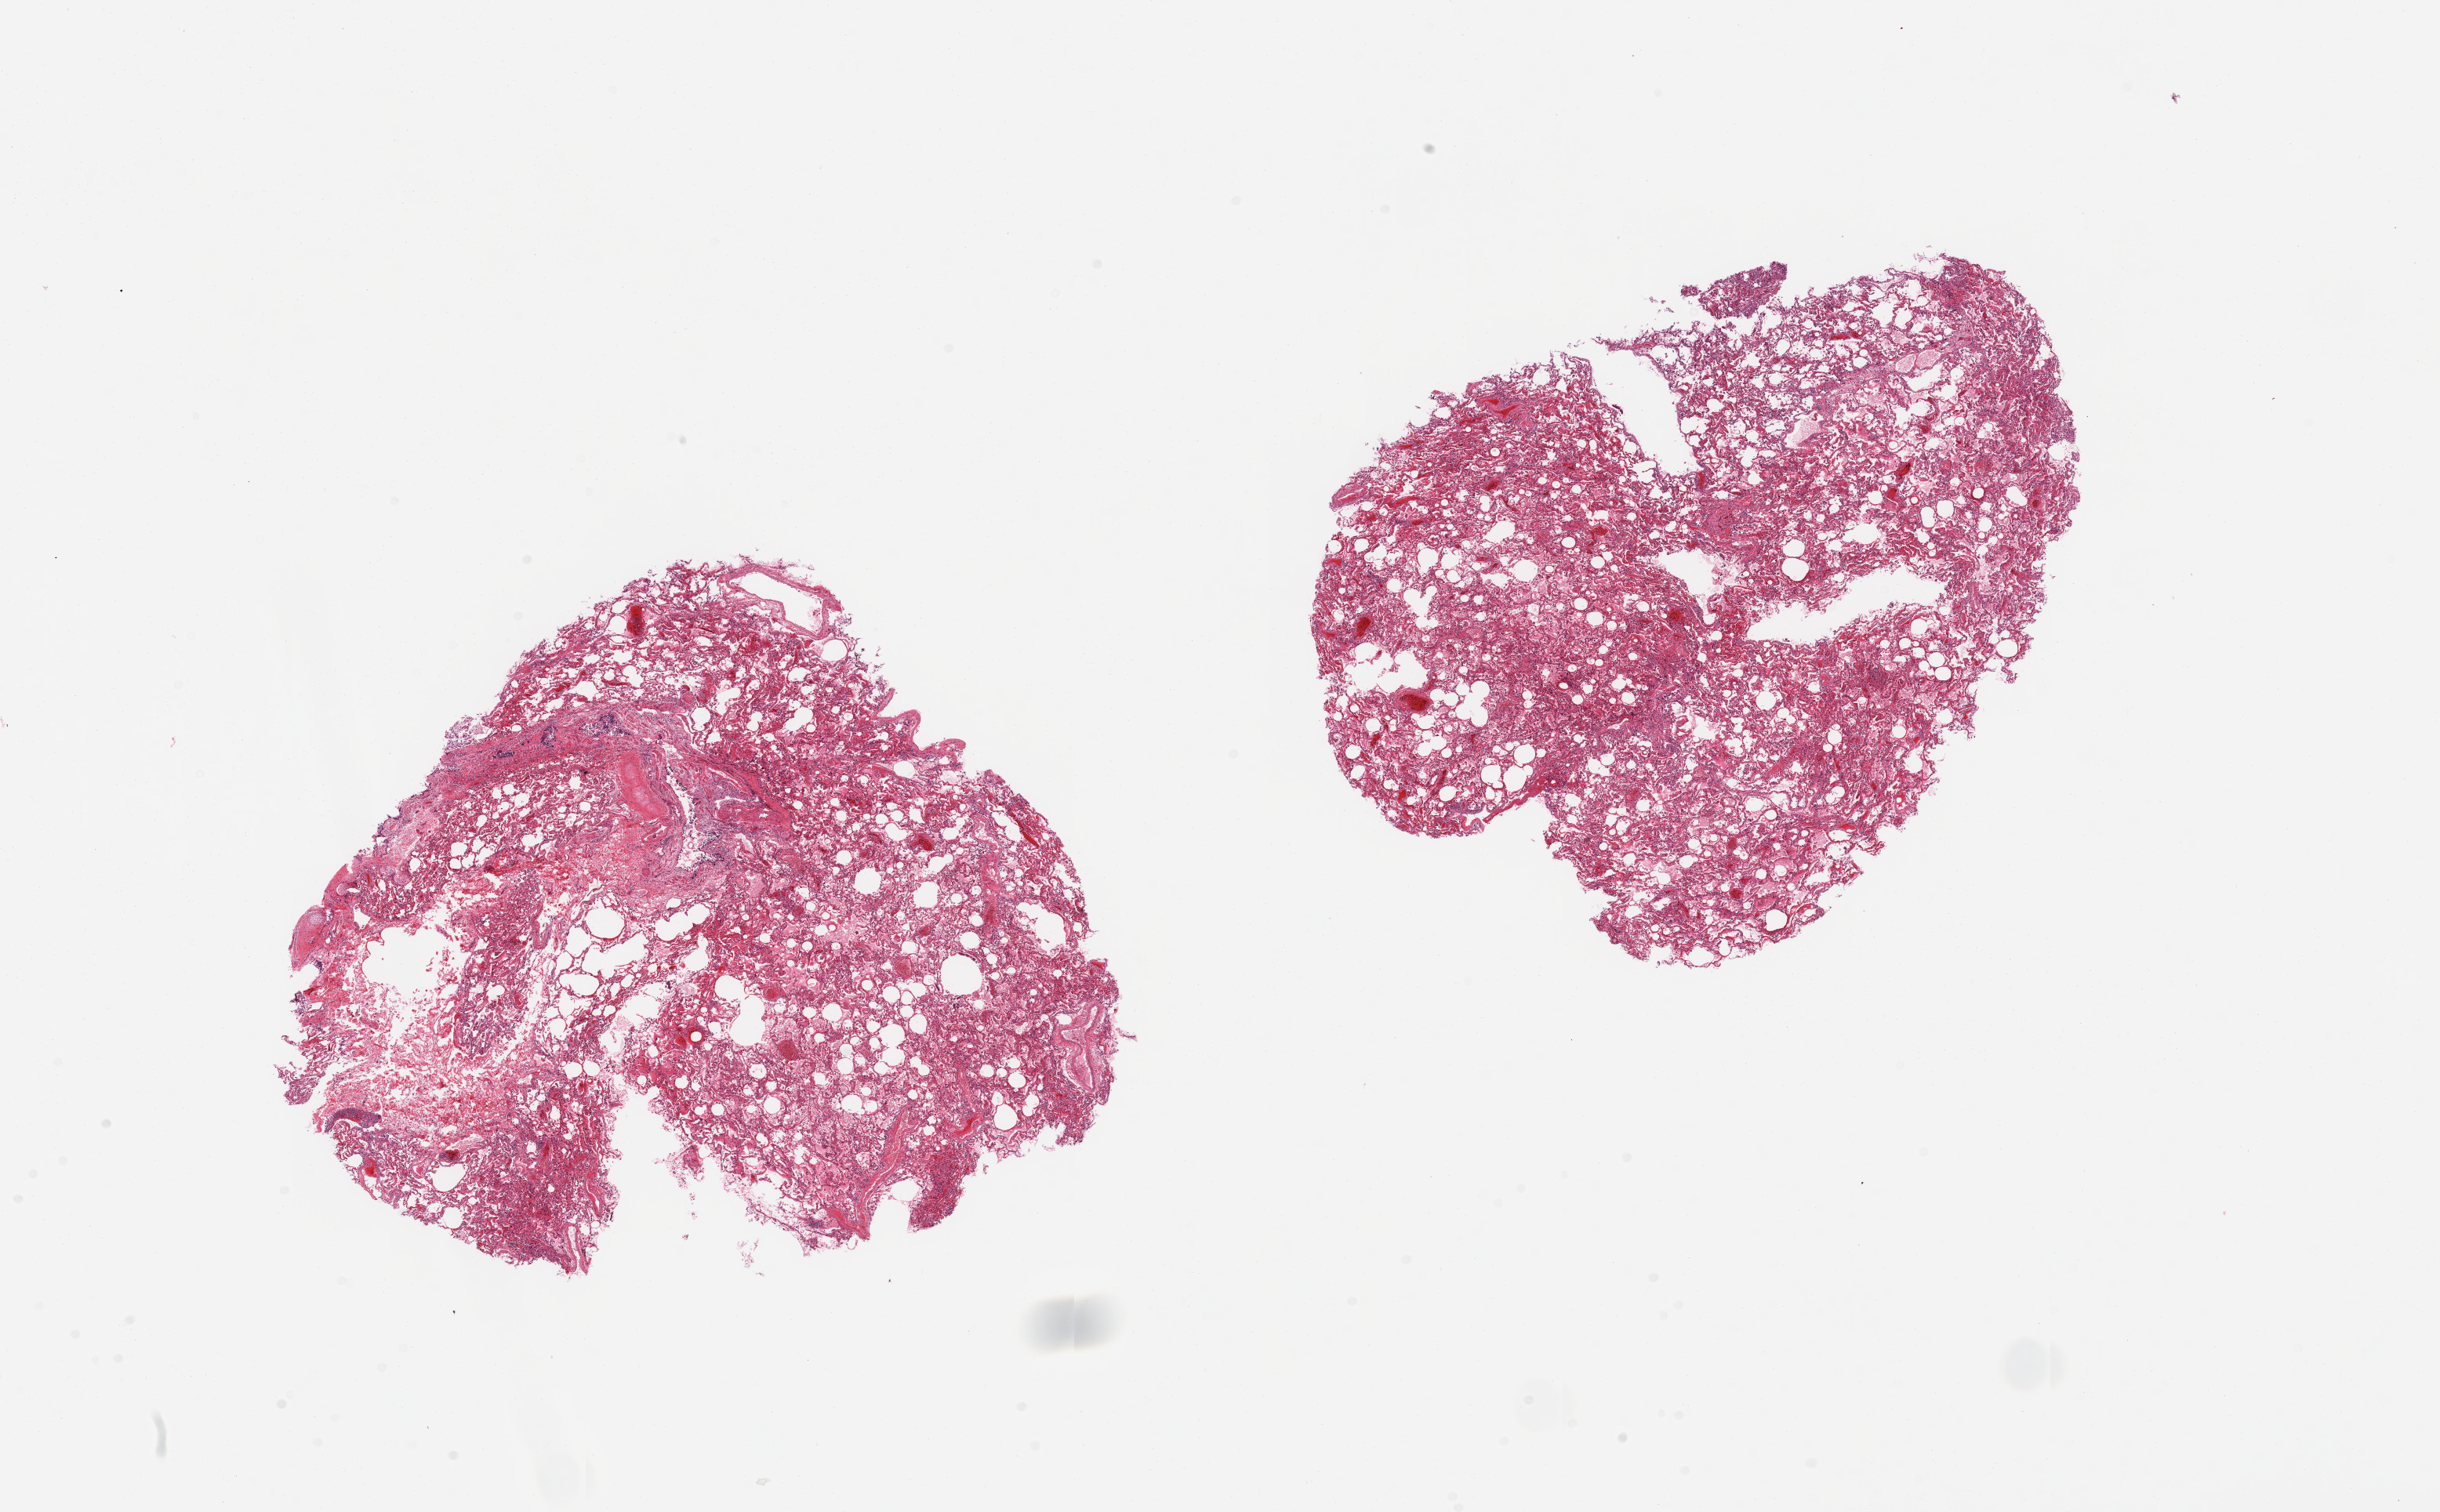
Haematoxylin and eosin whole-slide image, whole scanned area (about 24.6 x 15.3 mm, from a 20x scan) shown as a low-resolution overview; PAXgene-fixed, paraffin-embedded tissue; sampled site (target tissue): lung; tissue donor sample. Donor: male.
- pathologist's review note for this sample: 2 pieces, moderate congestion